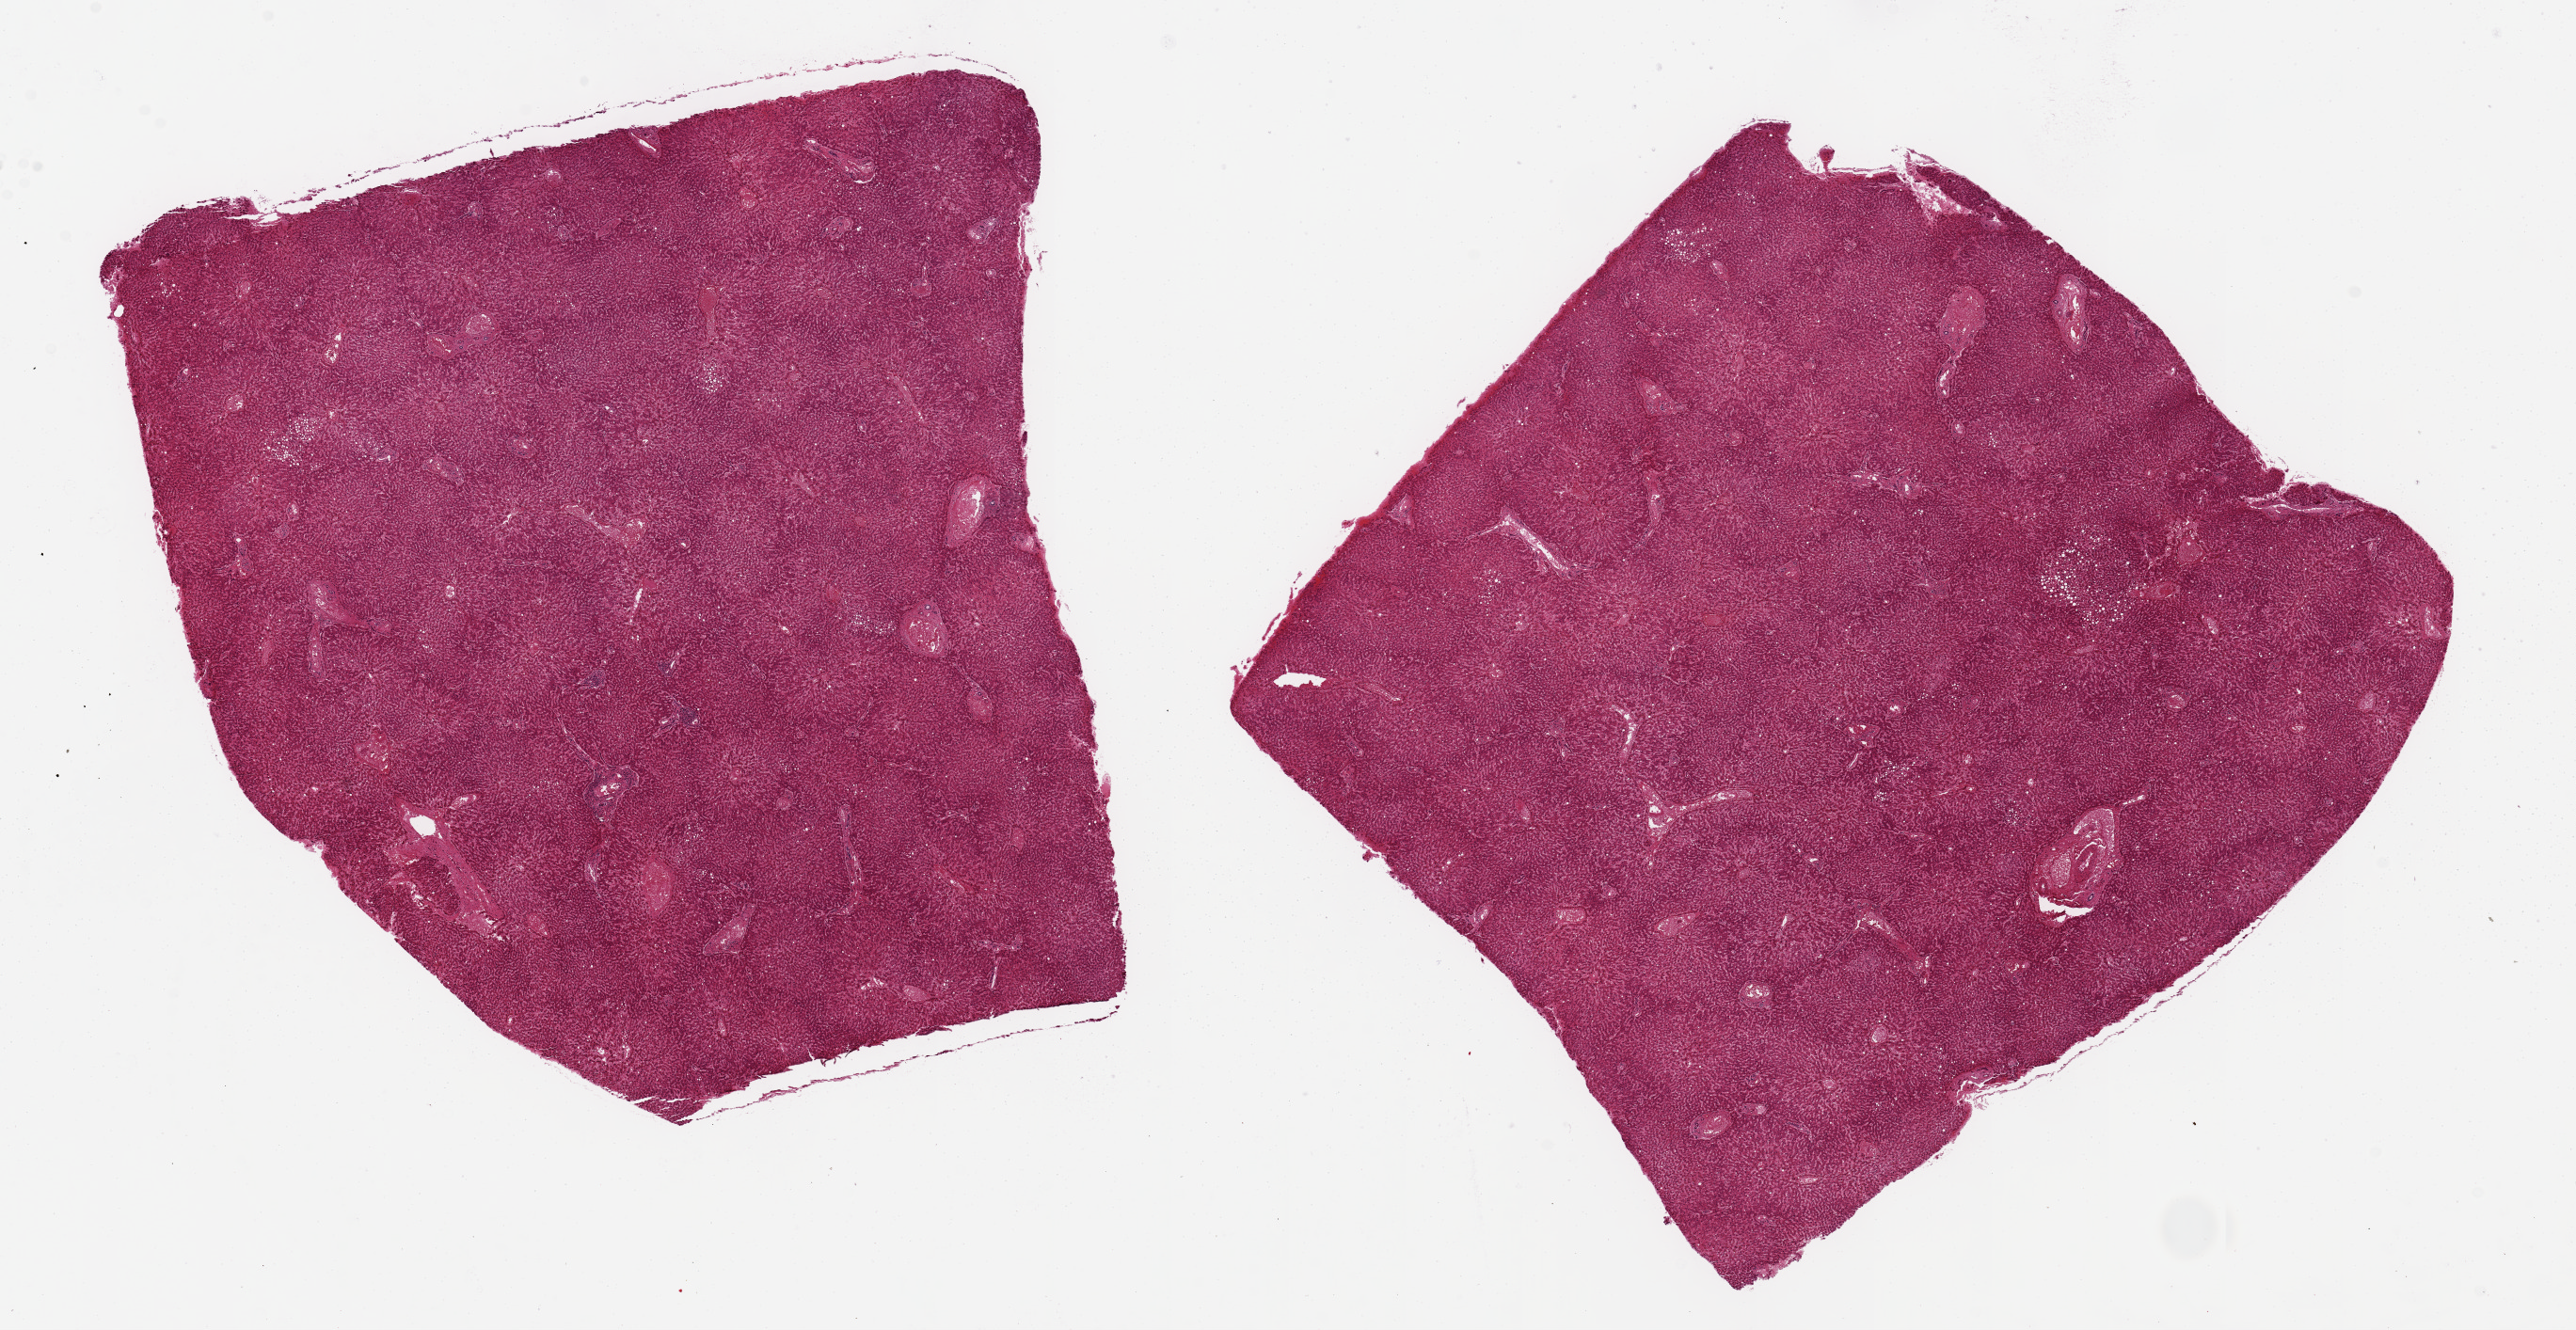
Digitized hematoxylin and eosin (H&E)-stained section — low-resolution overview of the scanned area, about 21.7 x 11.2 mm; PAXgene-fixed paraffin-embedded (PFPE) section; sampled site (target tissue): liver; tissue donor sample. Male donor.
Review note (as recorded): 2 ~8x7mm aliquots. Focal macrovesicular steatosis involves !0% of parenchyma.